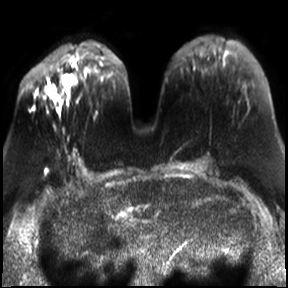
Breast MRI, one axial slice; position 11 of 30 along the scan axis; diffusion-weighted series; image 2 of 4 stored at this slice position (different b-values; order by instance number); 3 T; 4 mm slice thickness; 288 × 288 image matrix, field of view 340 × 340 mm. Female patient.
Outlined on this slice (expert manual segmentation):
- tumour on diffusion-weighted imaging: bounding box <63,75,74,85> (left, top, right, bottom; pixels)